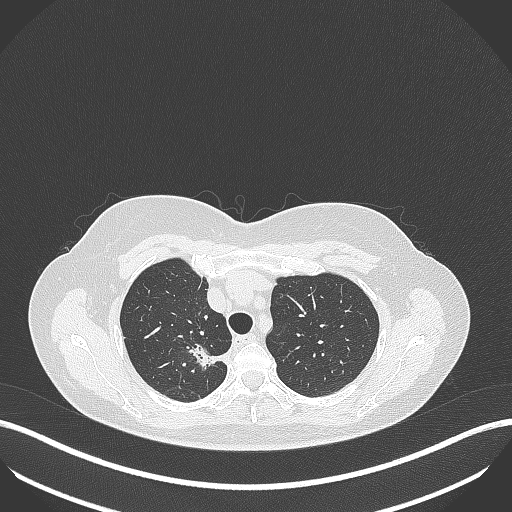
Chest CT, one axial slice; position 308 of 386 along the scan axis; 120 kVp; lung window (W 1500 / L -600 HU); 1 mm slice thickness; 512 × 512 image matrix, field of view 400 × 400 mm. Patient: female, 65 years. From the clinical record (not read from this slice): clinical TNM (as recorded): T1b N0 M0; histopathological grade: G2.
Outlined on this slice (rectangle marked by the reading radiologist):
- lung tumour (recorded histology: adenocarcinoma): bounding box [x1, y1, x2, y2] px = [188, 338, 230, 370]